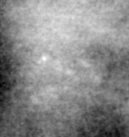
Cropped region of a digitized screen-film mammogram centred on a radiologist-marked abnormality; left breast; CC view.
- Marked abnormality: calcifications, morphology pleomorphic, distribution clustered; BI-RADS assessment category 4; subtlety rating 2 on a 1 (subtle) to 5 (obvious) scale; pathology result (as recorded, not read from the image): benign.